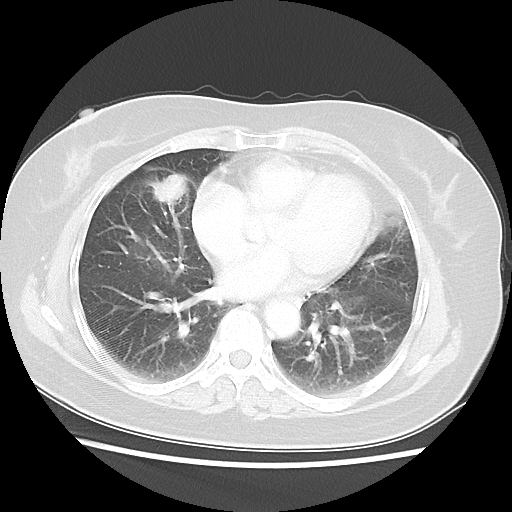
Chest CT, one axial slice. Position 21 of 48 along the scan axis. Lung window (W 1500 / L -600 HU). 5 mm slice thickness. 512 × 512 image matrix, field of view 343 × 343 mm. Female patient, age 61 years. From the clinical record (not read from this slice): clinical TNM (as recorded): T1c N0 M0.
Outlined on this slice (rectangle marked by the reading radiologist):
- lung tumour (recorded histology: adenocarcinoma): box from (x=145, y=171) to (x=189, y=206) px